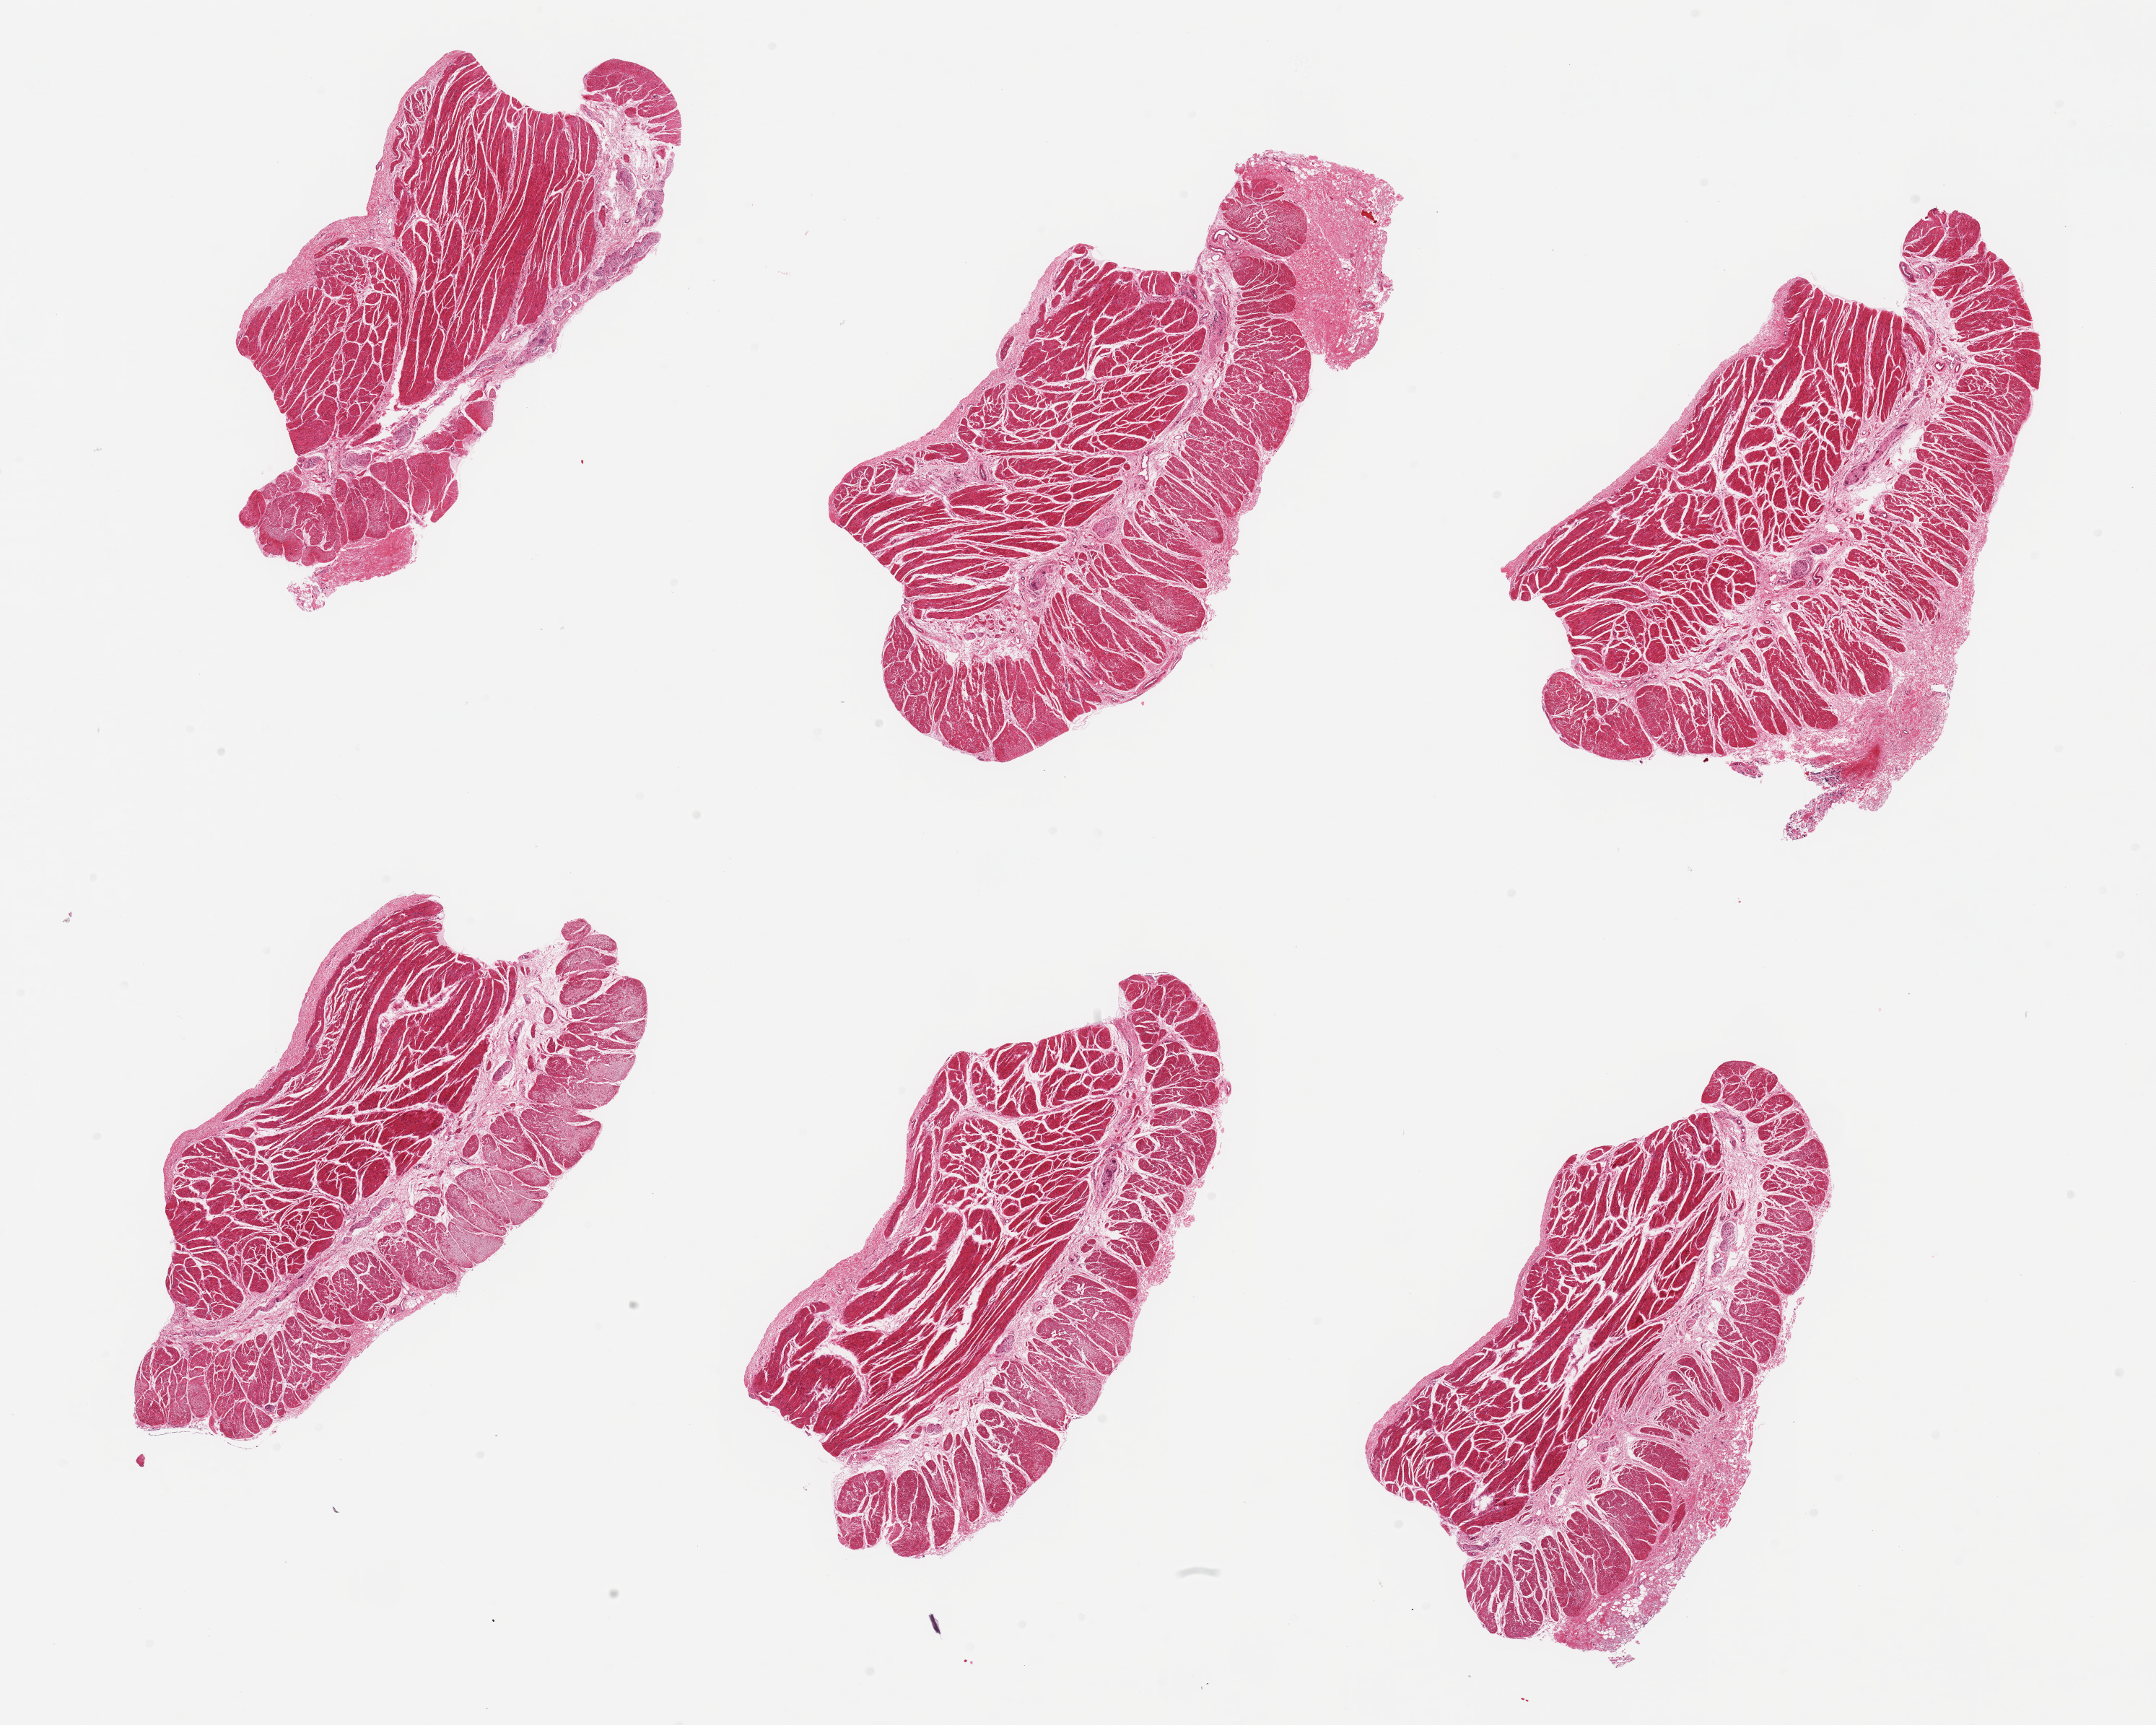
Whole-slide image, hematoxylin and eosin (H&E) stain, brightfield — a low-resolution overview of the entire scanned area, about 23.6 x 18.9 mm (acquisition: 20x scan), PAXgene-fixed paraffin-embedded (PFPE) section, sampled site (target tissue): esophageal muscle, tissue donor sample. Donor: female.
• pathologist's review note for this sample: 6 pieces; well dissected muscularis